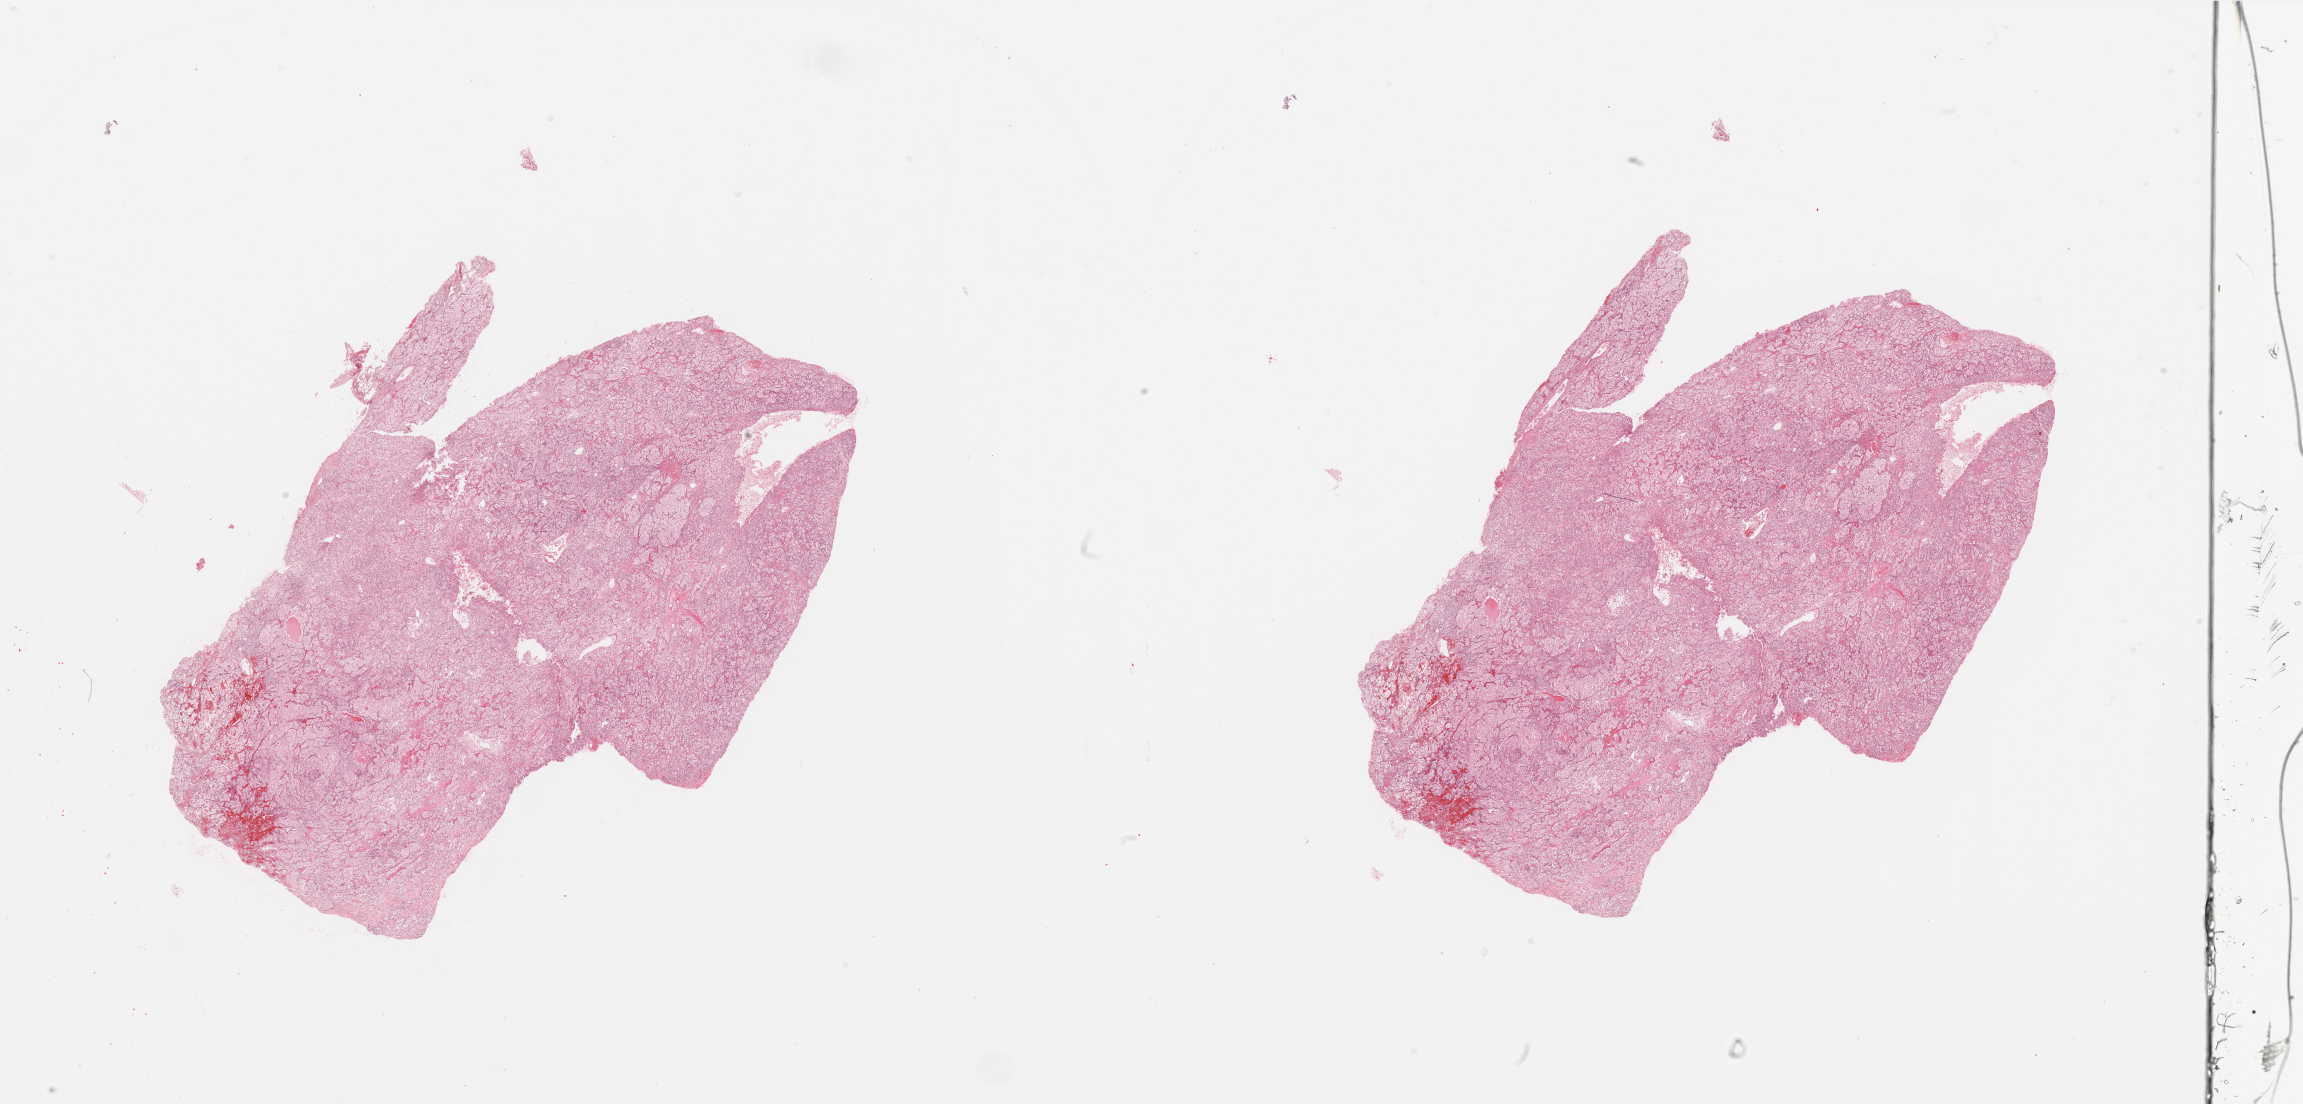
Hematoxylin and eosin (H&E) stained whole-slide image, a low-resolution overview of the entire scanned area, about 36.4 x 17.5 mm. Tumour tissue sample, sampled site: kidney. 56-year-old male patient. Histologic grade: G2 (moderately differentiated). Composition of this section per pathologist review: tumour nuclei 90%, necrosis 5%.
Histologic diagnosis: Renal cell carcinoma, NOS. AJCC pathologic stage: III.